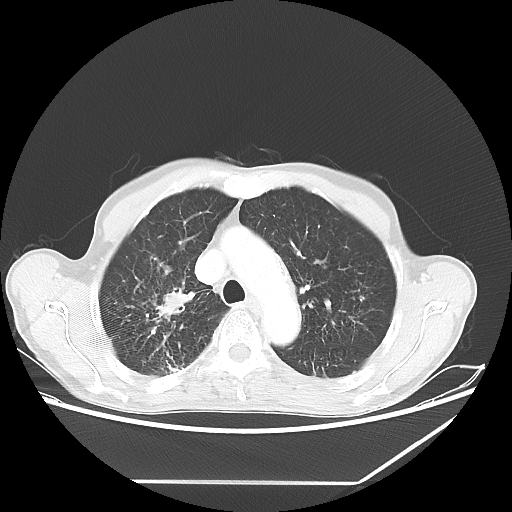
Chest CT, one axial slice. Slice 47 of 65 in the series (ordered by position). Lung window (W 1500 / L -600 HU). 5 mm slice thickness. 512 × 512 image matrix, field of view 397 × 397 mm. Male patient, age 68 years. Case-level facts recorded for this patient, not image findings: clinical TNM (as recorded): T3 N3 M0.
Outlined on this slice (bounding box drawn by a radiologist):
- lung tumour (recorded histology: adenocarcinoma): bounding box [x1, y1, x2, y2] px = [149, 280, 196, 328]